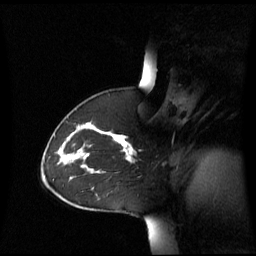
Breast MRI (dynamic contrast-enhanced), one sagittal slice; position 42 of 60 along the scan axis; dynamic contrast-enhanced series, image 2 of 3 at this slice position (ordered by acquisition); 1.5 T; TE 4.2 ms, TR 8.4 ms; 2.8 mm slice thickness; 256 × 256 image matrix. Patient: female, 43 years. Case-level facts recorded for this patient, not image findings: setting: breast cancer imaged before/during neoadjuvant chemotherapy; receptor status: triple-negative.
Structures marked on this image (semi-automatically segmented with operator editing):
- analysis volume of interest (the breast-tissue region the enhancement analysis was run in; not a lesion): bounding box (x1, y1, x2, y2) in pixels: (55, 124, 136, 173)
- tumour enhancement mask (voxels above the 70 % enhancement threshold inside the analysis volume of interest): (71, 134, 135, 161)